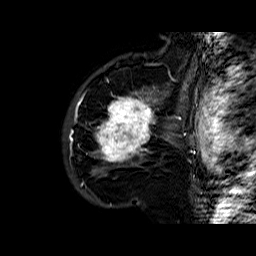
Breast MRI (dynamic contrast-enhanced), one sagittal slice. Slice 43 of 60 in the series (ordered by position). Dynamic contrast-enhanced series, time point 2 of 6 at this slice position (early post-contrast). 1.5 T. TE 6.4 ms, TR 32.8 ms. 256 × 256 image matrix, field of view 200 × 200 mm. Female patient. From the clinical record (not read from this slice): setting: breast cancer imaged before/during neoadjuvant chemotherapy; receptor status: HR-positive, HER2-negative.
Structures marked on this image (semi-automatic segmentation, software-assisted and operator-edited):
- analysis volume of interest (the breast-tissue region the enhancement analysis was run in; not a lesion): box from (x=86, y=77) to (x=163, y=177) px
- tumour enhancement mask (voxels above the 100 % enhancement threshold inside the analysis volume of interest): (x=95, y=92)–(x=157, y=163)